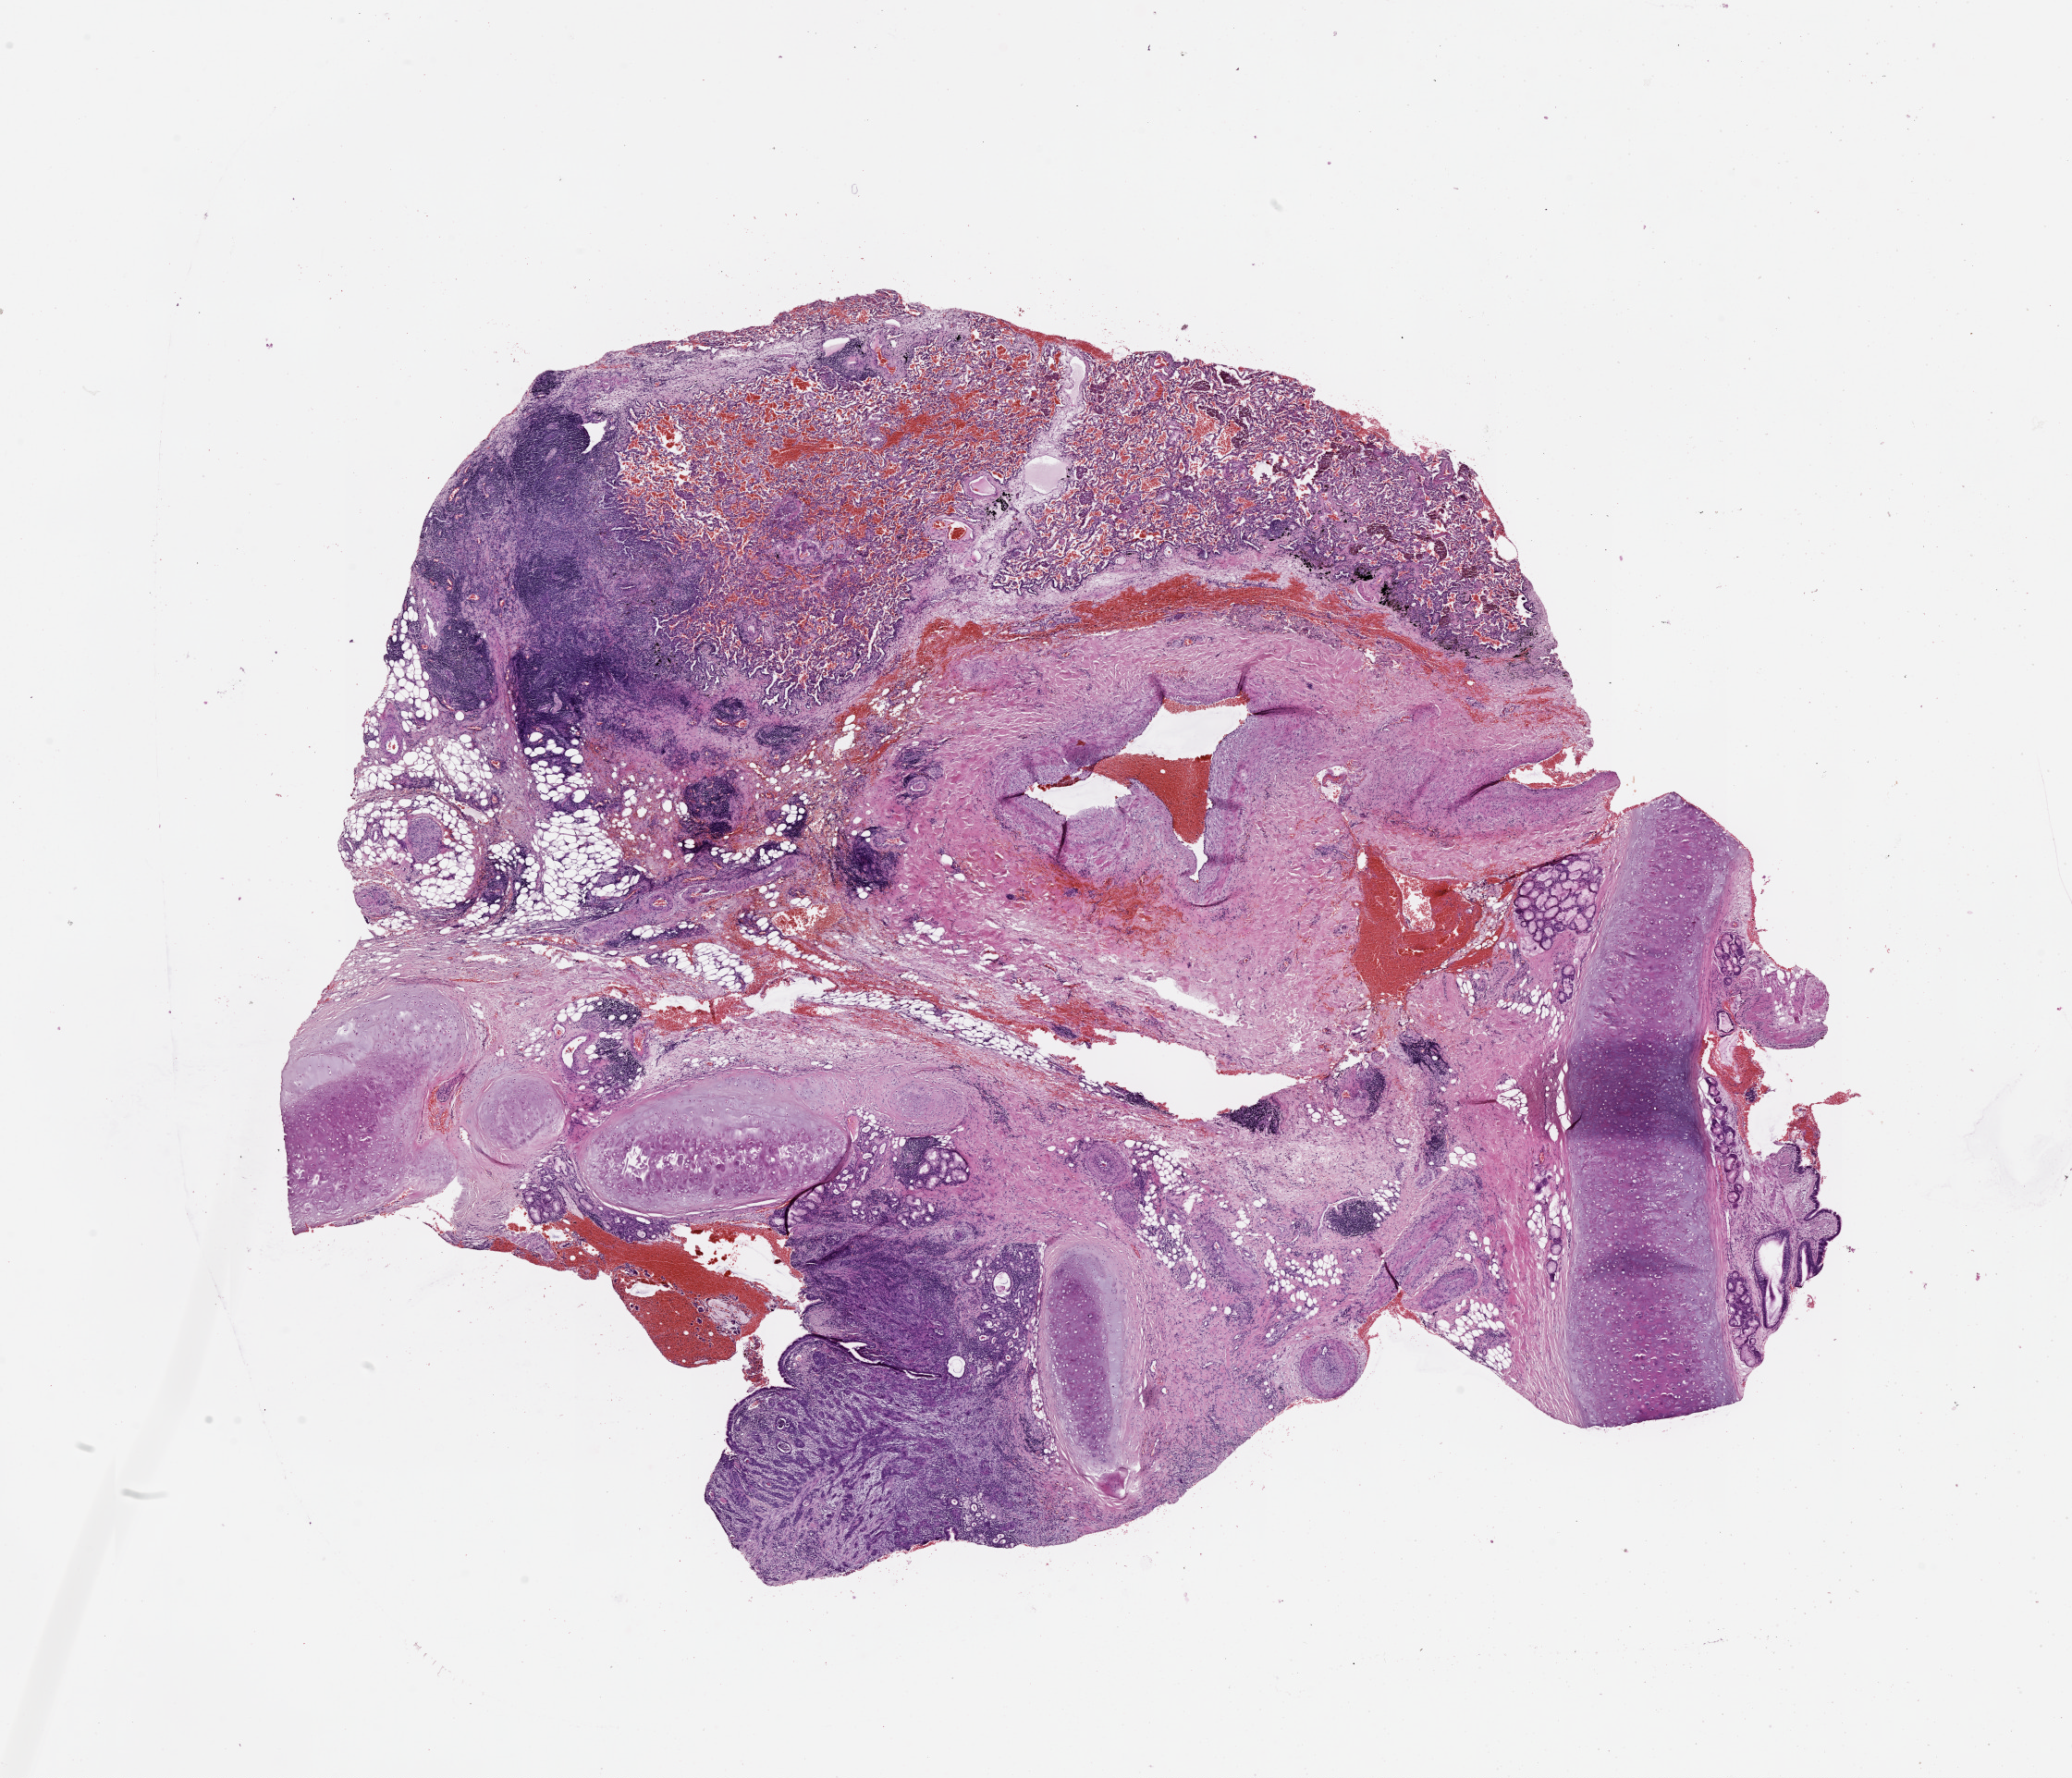
Digitized H&E tissue section (whole slide), whole scanned area (about 18.0 x 15.5 mm, slide scanned at 20x) shown as a low-resolution overview, lung, tumour tissue. 56-year-old female patient.
• patient diagnosis (cohort enrolment): squamous cell carcinoma (lung)